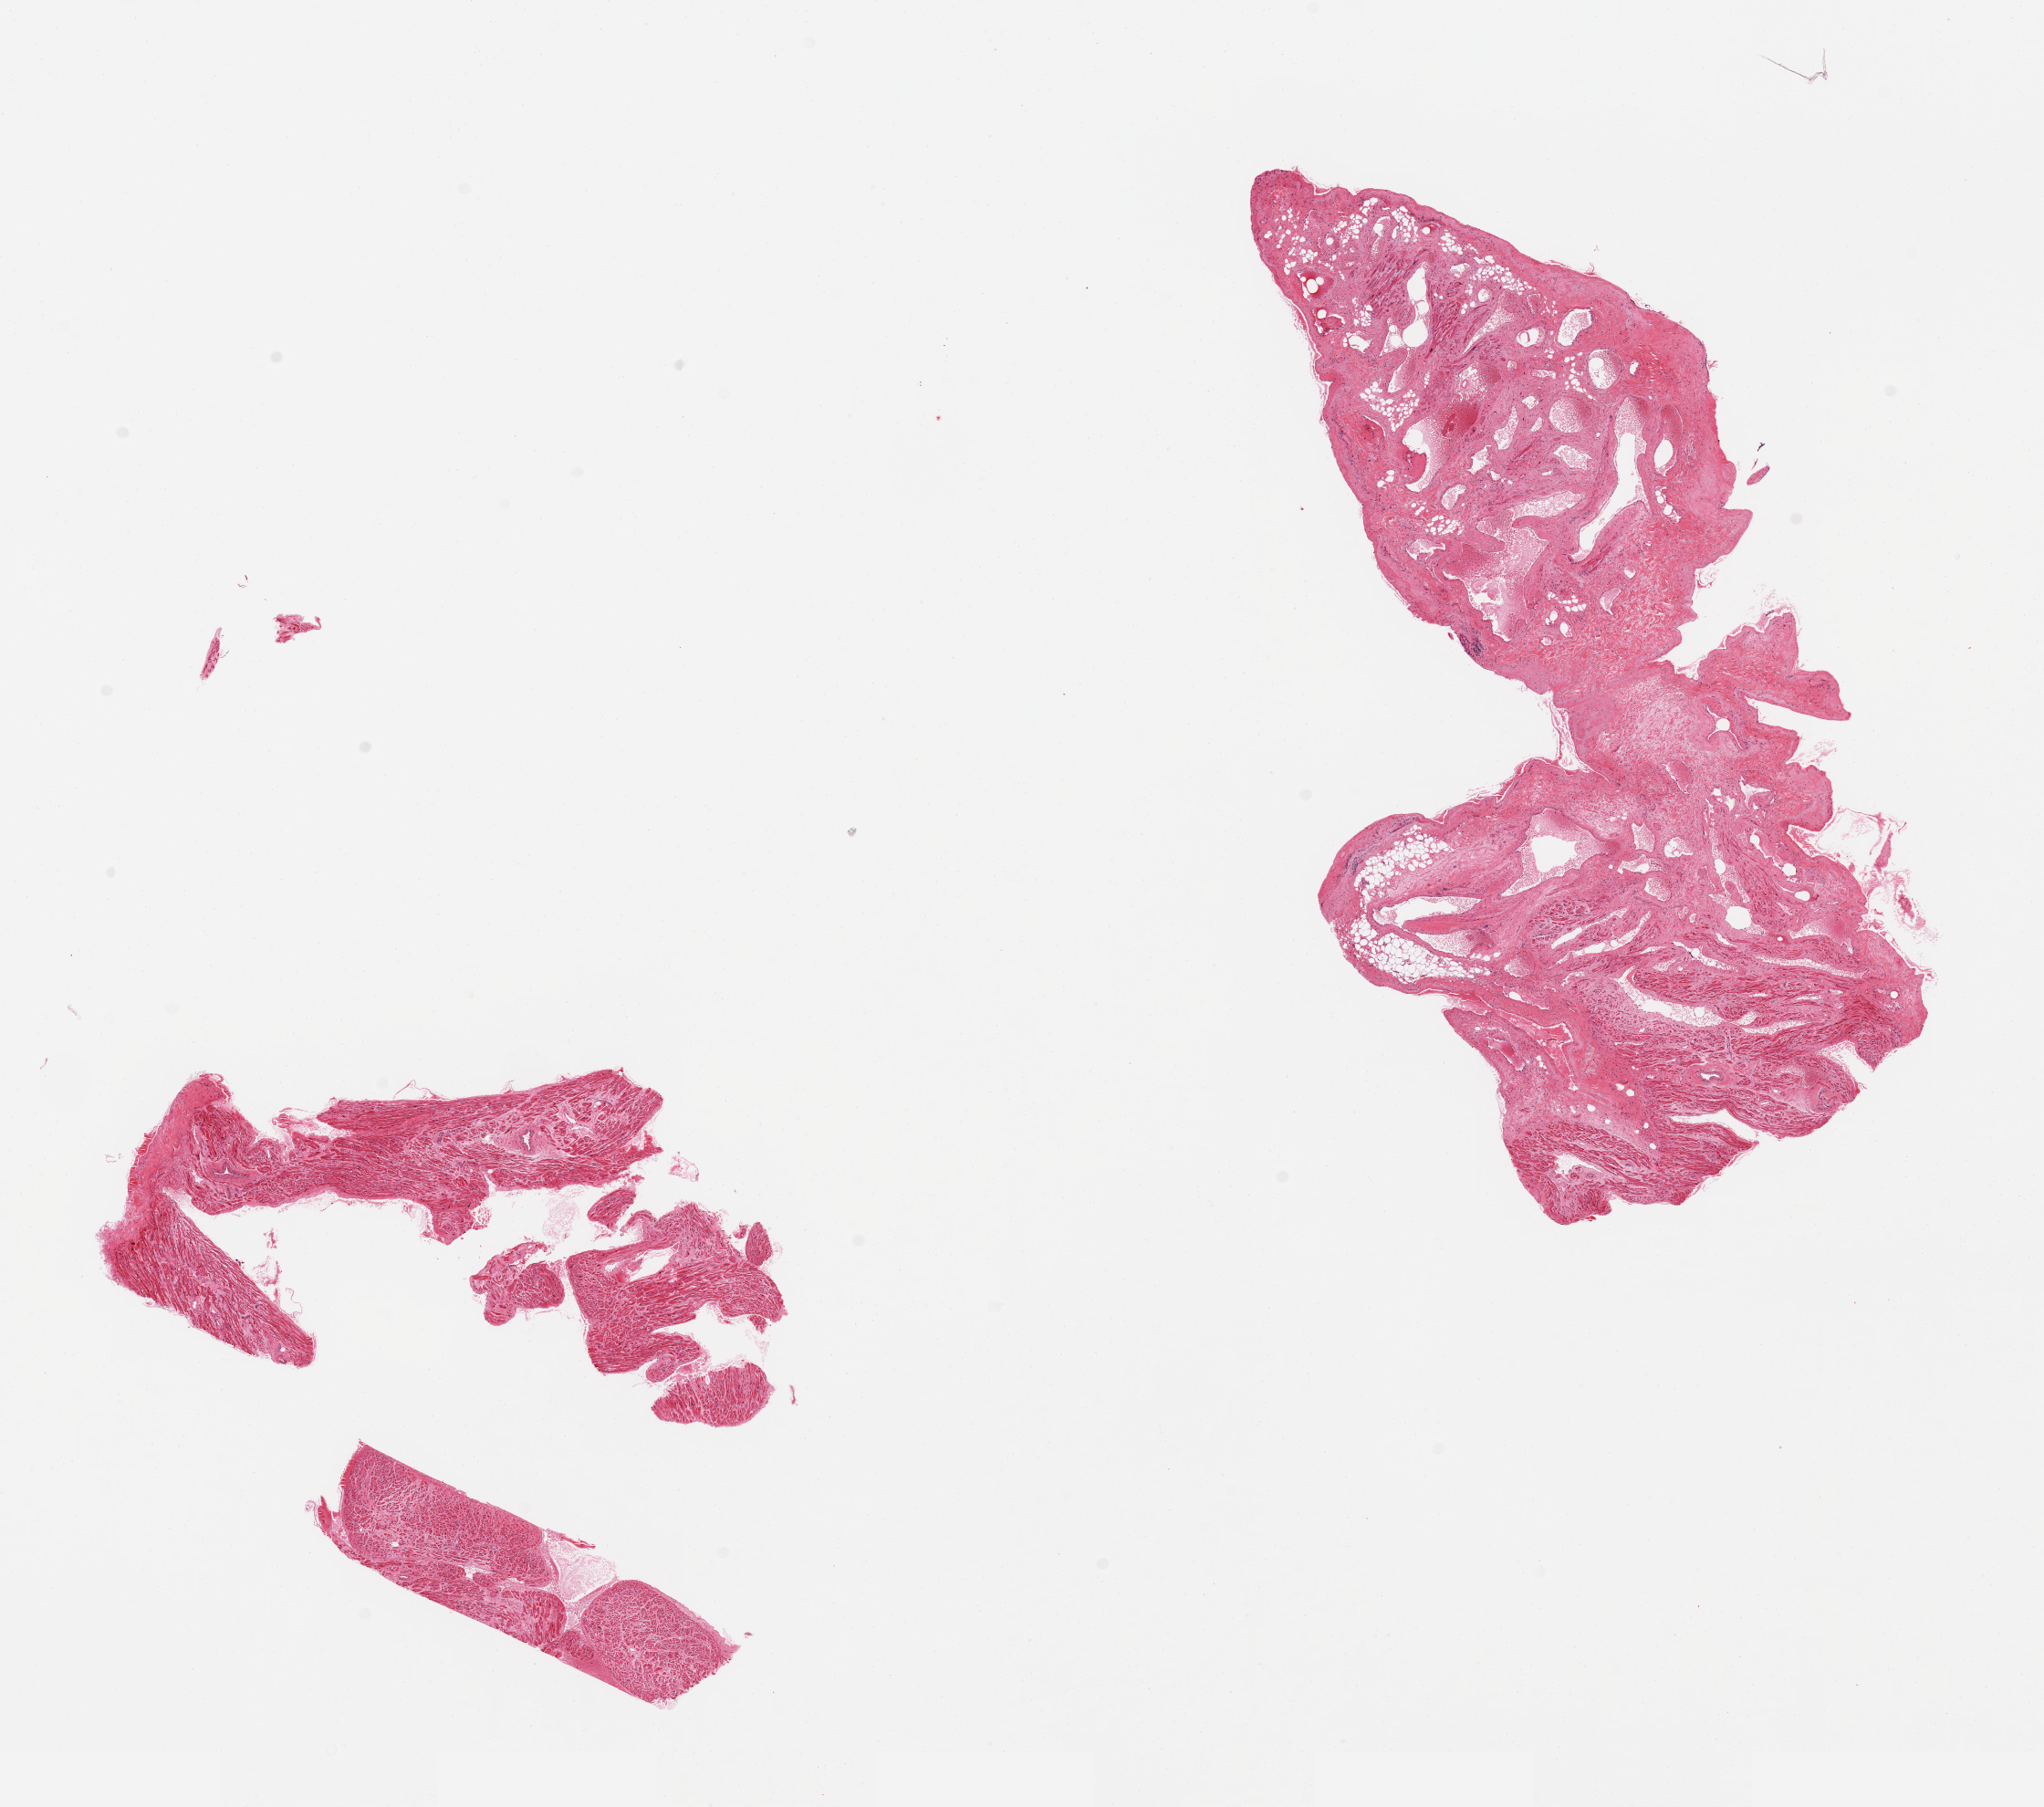
Whole-slide image, hematoxylin and eosin (H&E) stain — whole scanned area (about 17.7 x 15.7 mm, from a 20x scan) shown as a low-resolution overview. PAXgene-fixed, paraffin-embedded tissue. Section of auricular appendage (target tissue). Tissue donor sample. Donor sex: male.
* reviewer comment on this tissue sample: 3 pieces, one piece is predominantly fibrous/fat